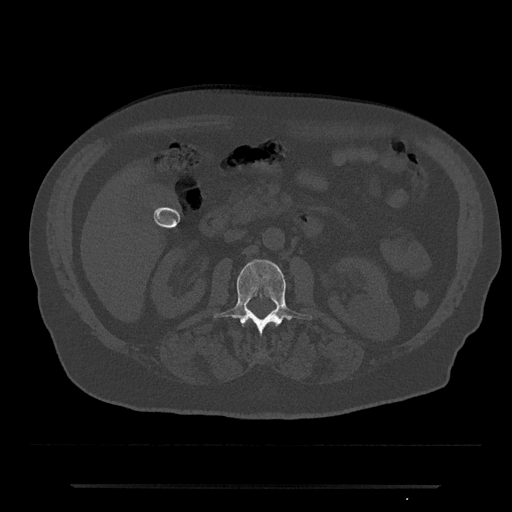
CT including the spine, one axial slice; position 476 of 797 along the scan axis; reconstruction kernel Br40s/3; 120 kVp; bone window (W 1800 / L 400 HU); 0.5 mm slice thickness; 512 × 512 image matrix, field of view 434 × 434 mm. Male patient, age 80 years. Case-level facts recorded for this patient, not image findings: primary cancer: prostate.
Structures marked on this image (semi-automatic segmentation, software-assisted and operator-edited):
- L2 vertebra: bounding box <214,259,312,336> (left, top, right, bottom; pixels)